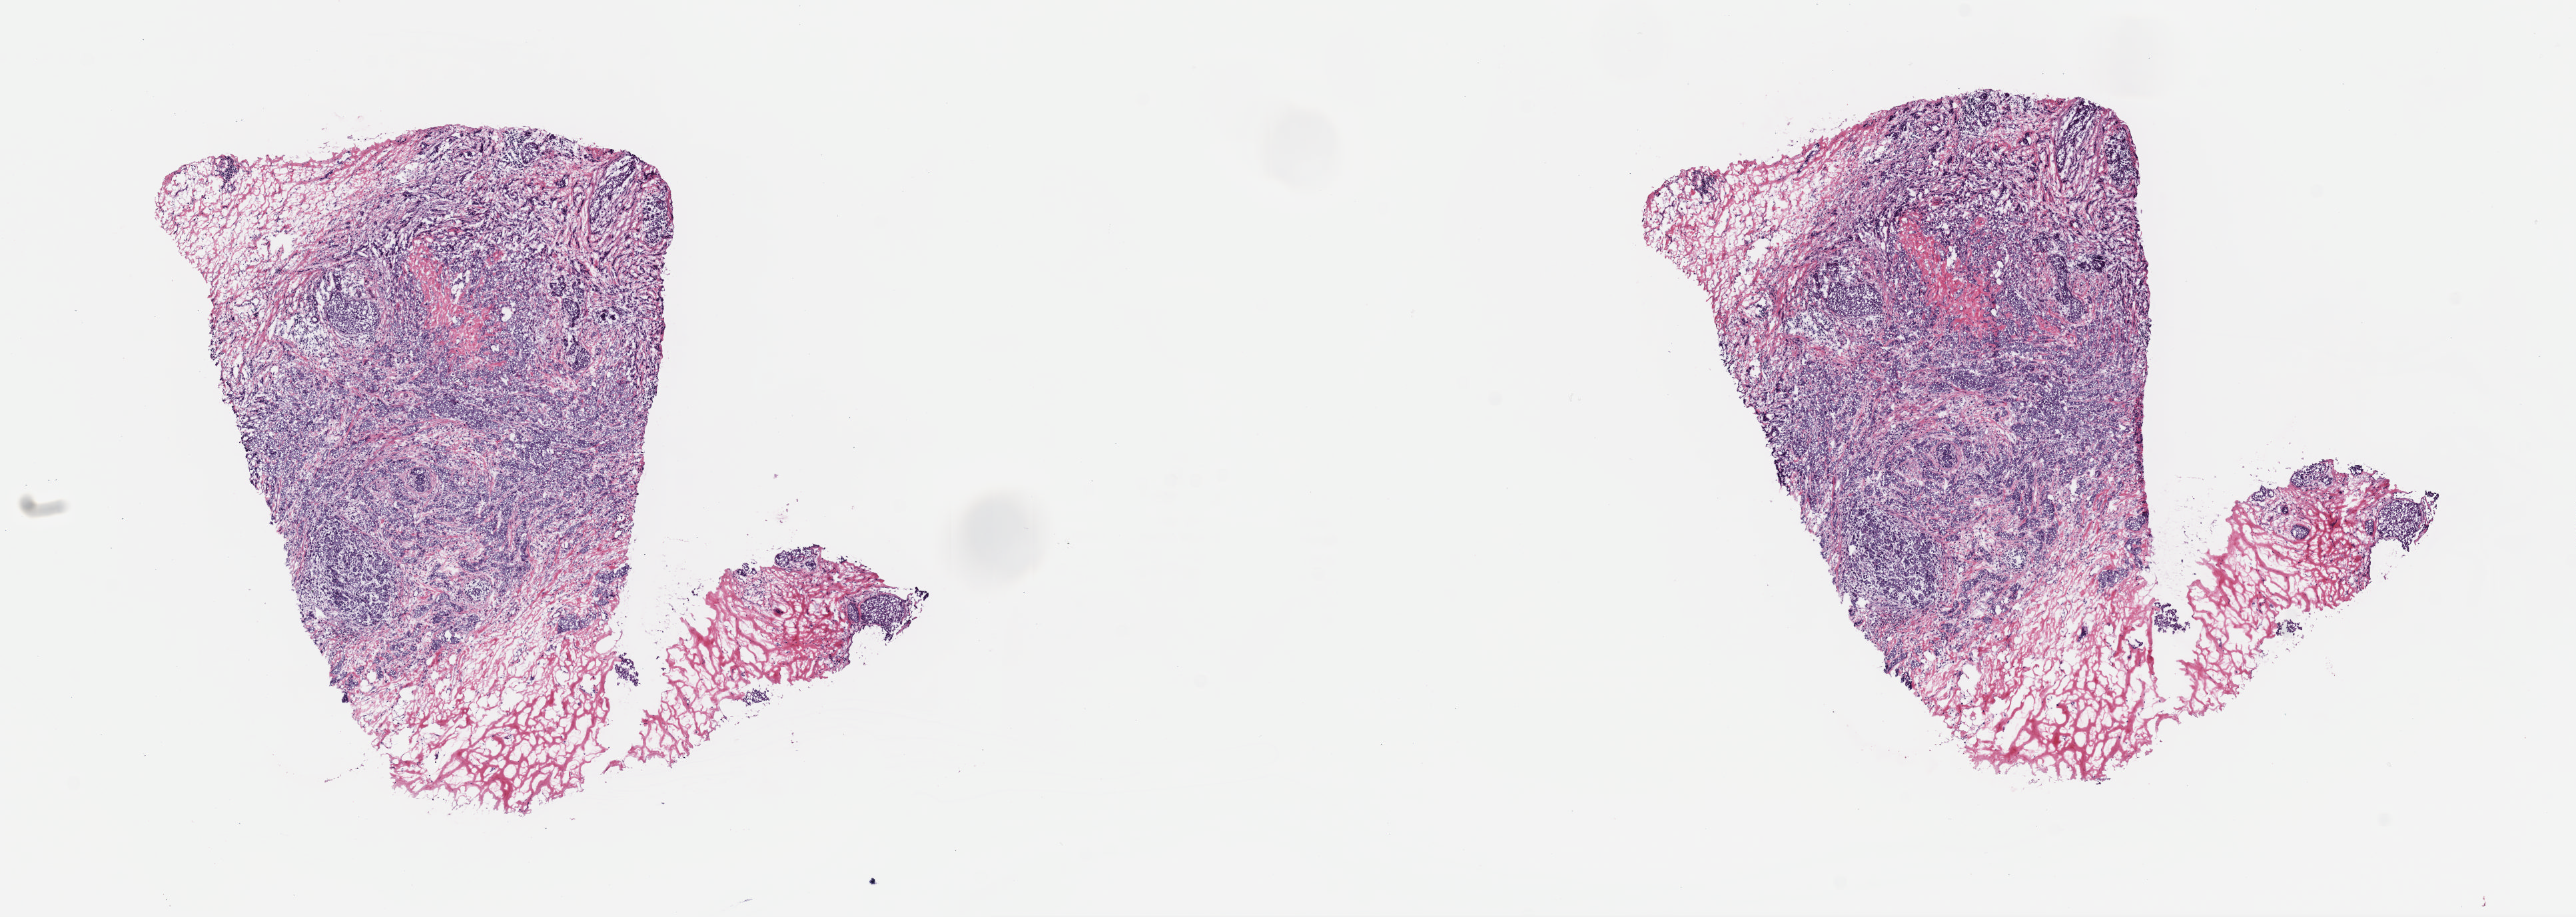
Digitized Hematoxylin and eosin (H&E) stained tissue section (whole slide), a low-resolution overview of the entire scanned area, about 15.3 x 5.4 mm (from a 40x scan). Frozen section from the top of the tissue portion. Sample: primary tumour, breast. Female, age 47 years at initial diagnosis. Slide review estimates, as recorded: tumour cells 90%, tumour nuclei 85%, normal cells 0%, stromal cells 10%, necrosis 0%. Inflammatory infiltration, as recorded: lymphocyte infiltration 0%, monocyte infiltration 0%, neutrophil infiltration 0%.
Lymph nodes positive (case pathology): 2 of 17 examined. AJCC pathologic stage: IIB. Diagnosis: Infiltrating duct carcinoma, NOS.